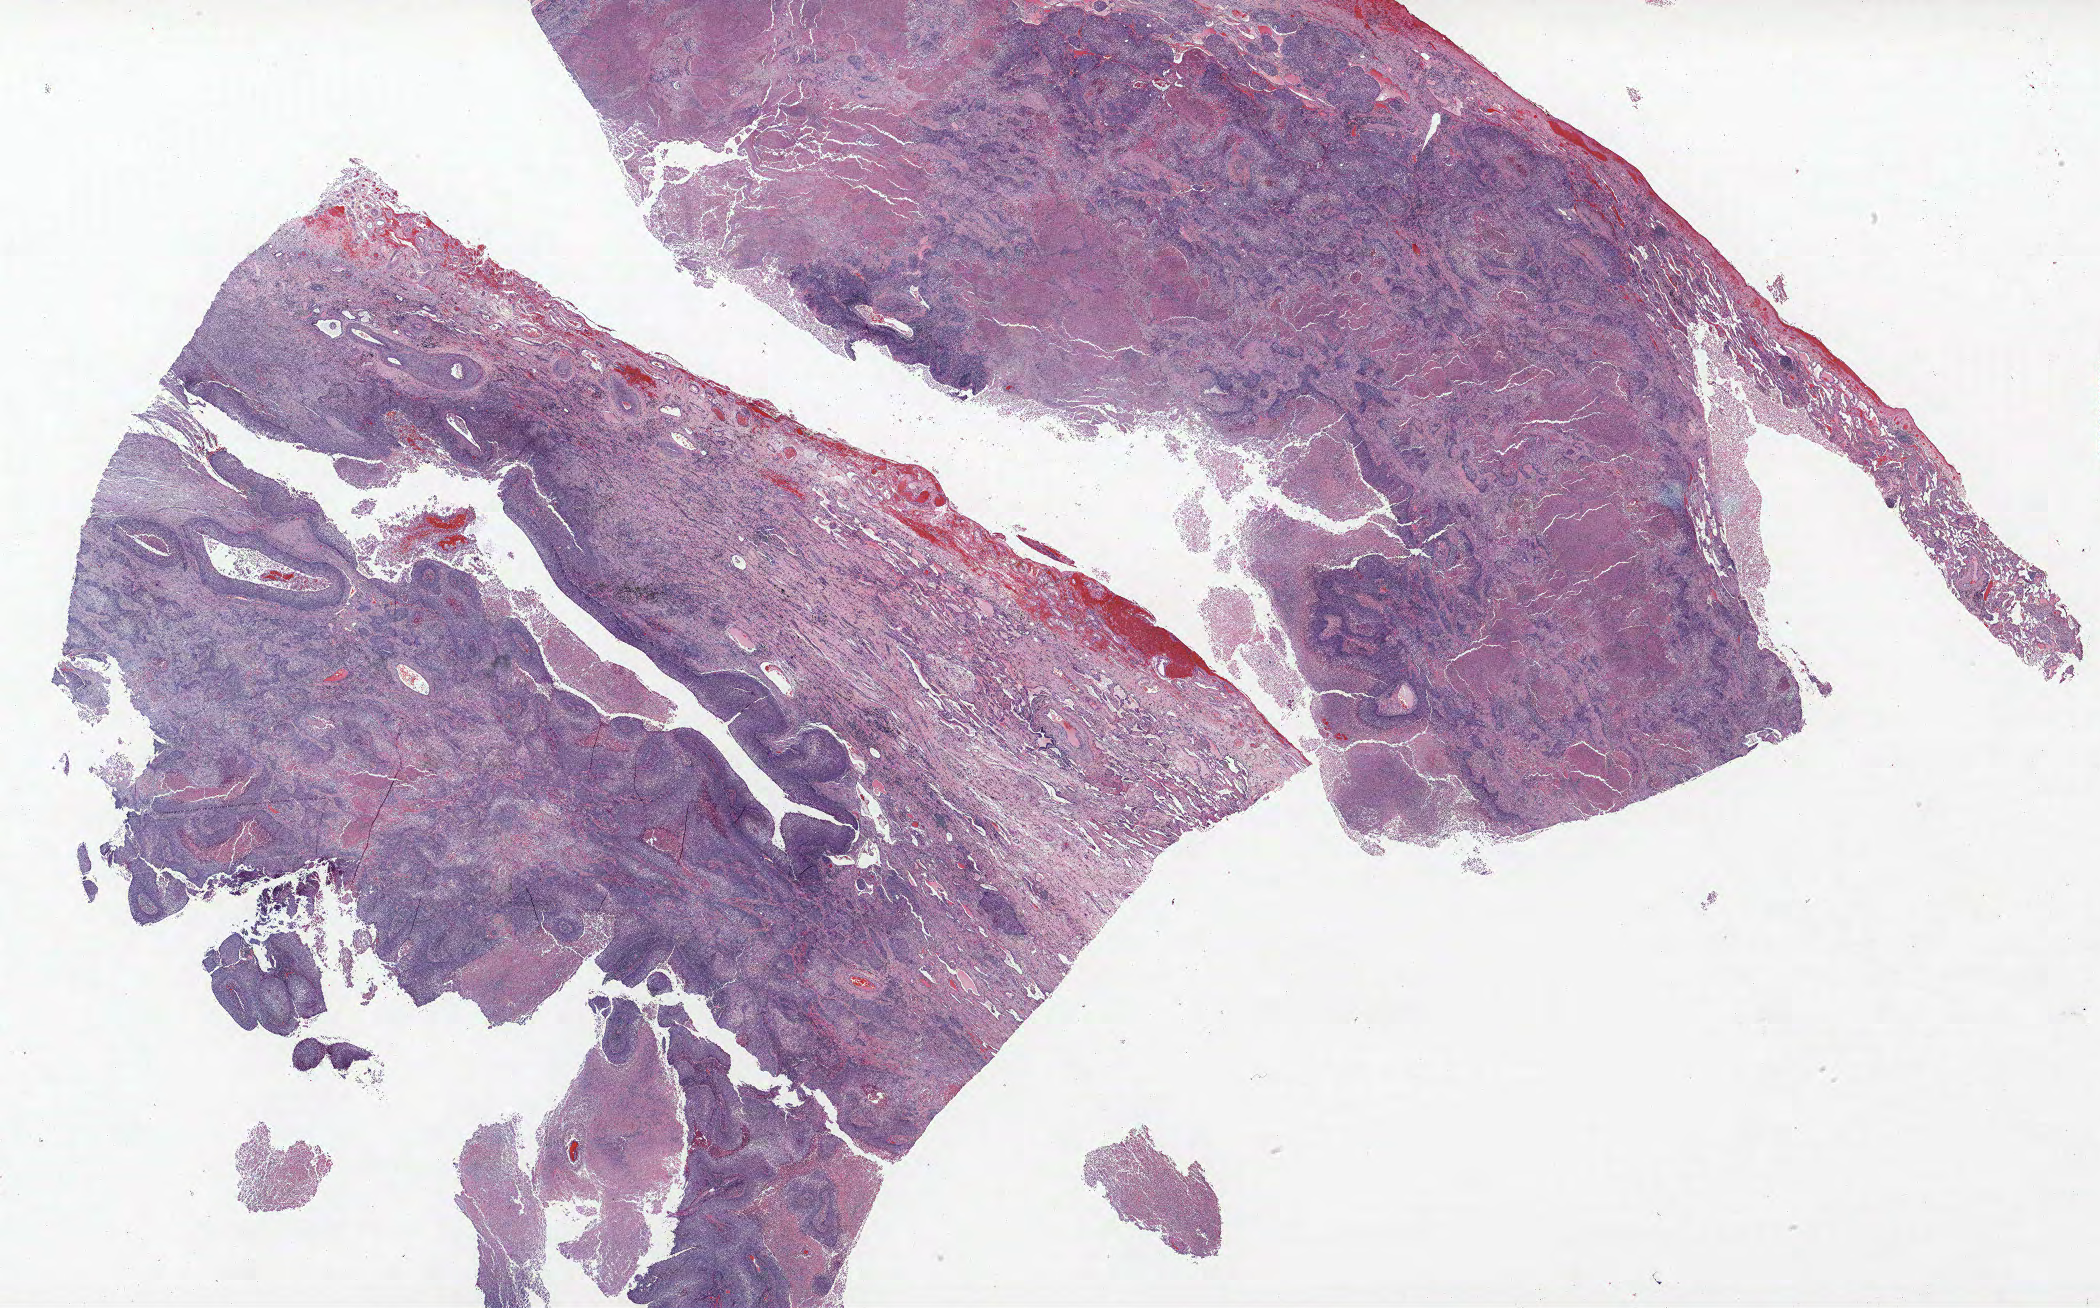
Whole-slide histology image, H&E — a low-resolution overview of the entire scanned area, about 33.6 x 20.9 mm (slide scanned at 40x), formalin-fixed paraffin-embedded (FFPE) section, lung tissue. Male patient, aged 71 at enrolment.
Participant's lung-cancer diagnosis: Squamous cell carcinoma, NOS (ICD-O-3 8070/3).